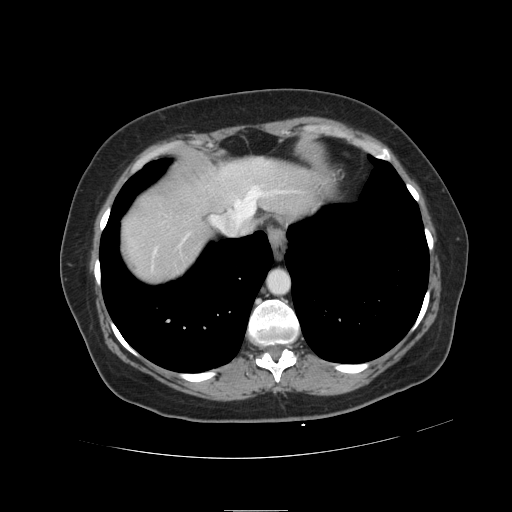
Contrast-enhanced abdominal CT, one axial slice. Slice 106 of 121 in the series (ordered by position). 120 kVp. Soft-tissue window (W 400 / L 40 HU). 512 × 512 image matrix, field of view 400 × 400 mm. Female patient, age 52 years. Case-level facts recorded for this patient, not image findings: diagnosis: colorectal cancer liver metastases, imaged before liver resection; multiple liver metastases: yes; largest metastasis: 6.3 cm; disease in both lobes: no.
Outlined on this slice (expert manual segmentation):
- hepatic veins: box from (x=152, y=186) to (x=285, y=270) px
- liver: (x=121, y=158)–(x=318, y=283)
- planned liver remnant (the part of the liver to remain after resection): (x=195, y=158)–(x=320, y=213)